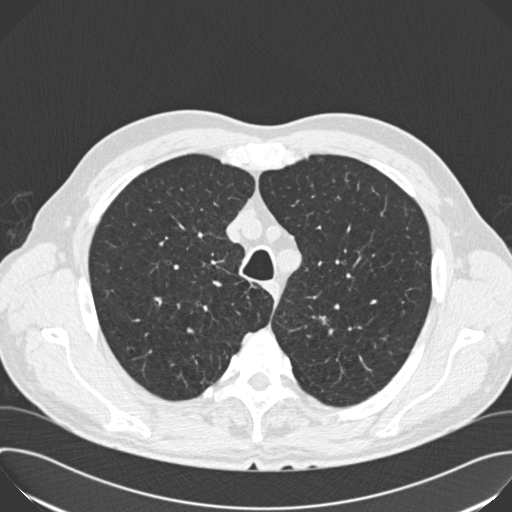
Axial slice from a low-dose chest CT screening exam; second screening round (one year after baseline); lung window (W 1500 / L -600 HU); 512 × 512 image matrix. Male participant, aged 66 years at enrolment. Current smoker at enrolment.
• Expert-annotated lung lesion, bounding box <302,300,347,343> (left, top, right, bottom; pixels).
• The exam's reader record, not a measurement of the box and not confirmed to be the same lesion: non-calcified nodule or mass ≥4 mm, left upper lobe, 8 × 7 mm, poorly defined margins, soft tissue attenuation, pre-existing on the prior screen: yes; interval growth: yes.
• Official screen result: positive, other.
• Later outcome: lung cancer diagnosed 390 days after this screen (after the third annual screen) — squamous cell carcinoma, NOS, left upper lobe, poorly differentiated (G3), stage IA (AJCC 6th edition), 15 mm at pathology.